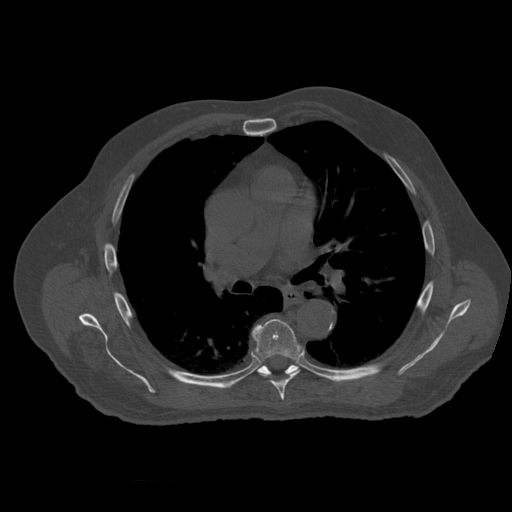
CT including the spine, one axial slice. Position 374 of 399 along the scan axis. 120 kVp. Bone window (W 1800 / L 400 HU). 512 × 512 image matrix. Patient age 73 years. From the clinical record (not read from this slice): primary cancer: prostate; vertebrae with lytic lesions (as recorded): L2.
Structures marked on this image (semi-automatically segmented with operator editing):
- T6 vertebra: bounding box [x1, y1, x2, y2] px = [252, 319, 301, 401]
- T7 vertebra: [258, 365, 301, 377]